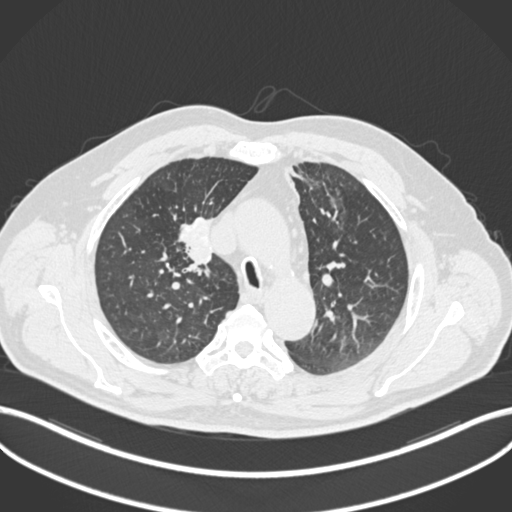
Chest CT, one axial slice; position 141 of 255 along the scan axis; reconstruction kernel B30f; 120 kVp; lung window (W 1500 / L -600 HU); 512 × 512 image matrix, field of view 400 × 400 mm. Patient: male, 60 years. From the clinical record (not read from this slice): clinical TNM (as recorded): T1b N1 M0.
Structures marked on this image (rectangle marked by the reading radiologist):
- lung tumour (recorded histology: squamous cell carcinoma): bounding box [x1, y1, x2, y2] px = [171, 217, 219, 272]